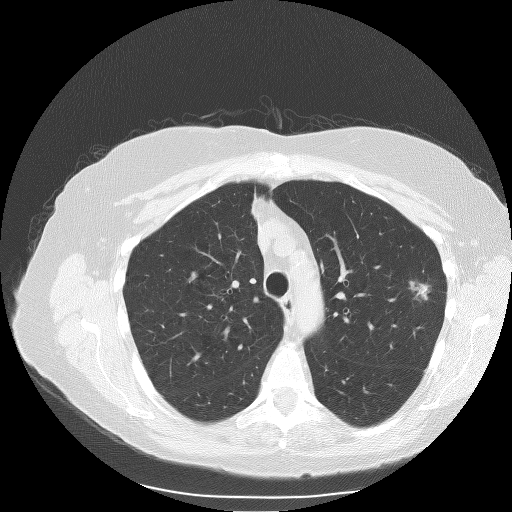
Chest CT (low-dose screening protocol), one axial image, first (baseline) screen, lung window (W 1500 / L -600 HU), 512 × 512 image matrix, field of view 360 × 360 mm. Female, age 71 years at enrolment.
Lesion marked by an expert reader, box from (x=401, y=276) to (x=443, y=313) px. Reader record for this screening exam (exam-level; its link to the box is not recorded): non-calcified nodule or mass ≥4 mm, left upper lobe, 15 × 9 mm, spiculated (stellate) margins, soft tissue attenuation. Later outcome: lung cancer diagnosed 77 days after this screen — adenocarcinoma, NOS, left upper lobe, moderately differentiated (G2), stage IA (AJCC 6th edition), 15 mm at pathology.